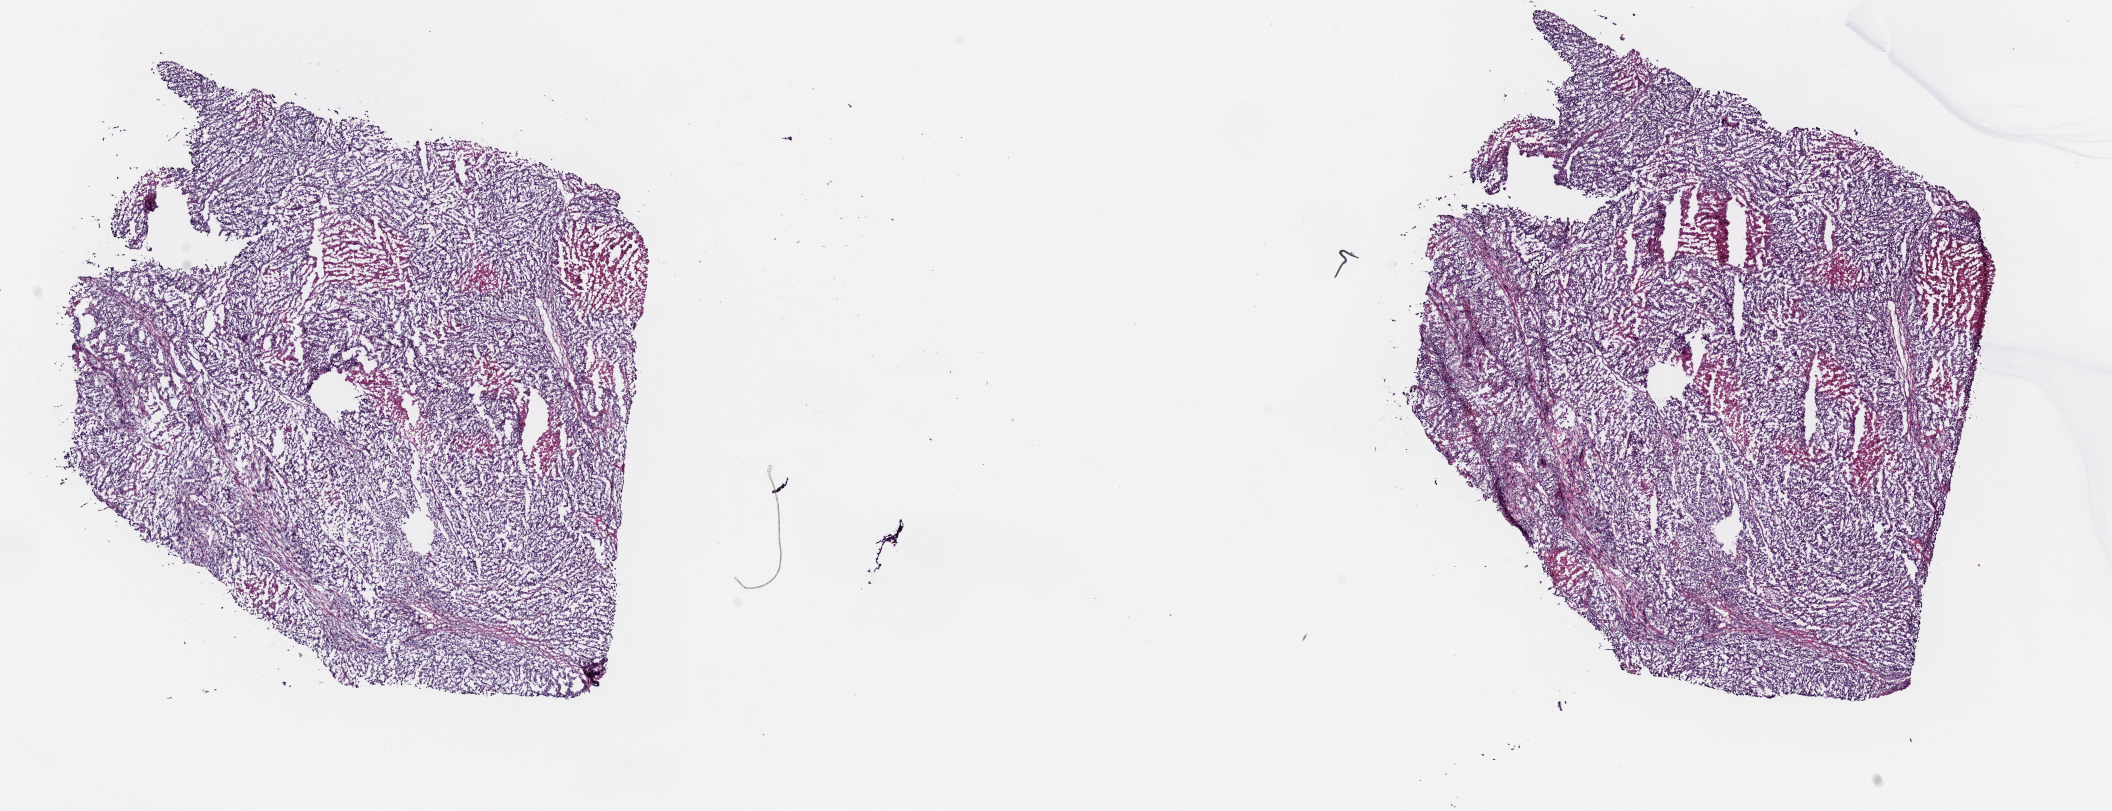
Whole-slide histology image, H&E — whole scanned area (about 16.7 x 6.4 mm, acquisition: 40x scan) shown as a low-resolution overview, frozen section from the top of the tissue portion, metastatic tumour sample, sampled site: pelvic lymph nodes. Male patient; age at initial diagnosis 53 years. Composition of this section per pathologist review: tumour cells 90%, tumour nuclei 90%, normal cells 0%, stromal cells 0%, necrosis 10%. Infiltration values recorded for this section: lymphocyte infiltration 0%, monocyte infiltration 0%, neutrophil infiltration 0%.
This section: metastatic tumour tissue. Patient diagnosis: Malignant melanoma, NOS.